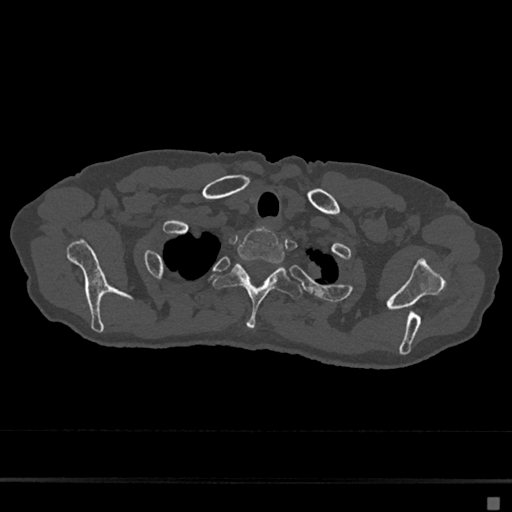
CT including the spine, one axial slice. Slice 587 of 797 in the series (ordered by position). Reconstruction kernel Br40s/3. 120 kVp. Bone window (W 1800 / L 400 HU). 0.5 mm slice thickness. 512 × 512 image matrix, field of view 360 × 360 mm. Patient: female, 68 years. Case-level facts recorded for this patient, not image findings: primary cancer: renal.
Outlined on this slice (semi-automatically segmented with operator editing):
- T1 vertebra: box from (x=237, y=228) to (x=285, y=263) px
- T2 vertebra: (x=213, y=263)–(x=303, y=330)